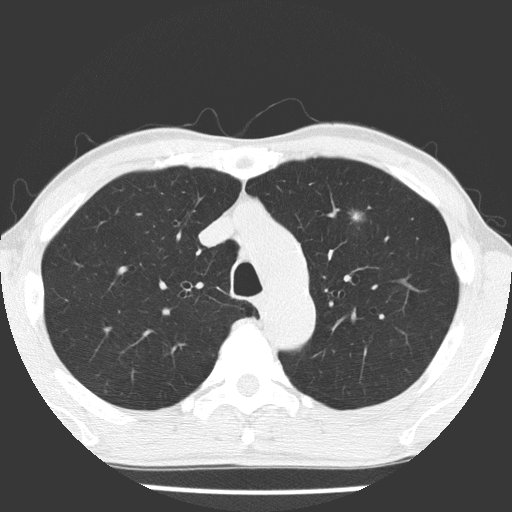
Axial slice from a low-dose chest CT screening exam; baseline annual screen; lung window (W 1500 / L -600 HU); 120 kVp; slice 51 of 177 in the series. Male participant, aged 66 years at enrolment.
Expert reader's lesion annotation, bounding box <330,197,378,242> (left, top, right, bottom; pixels). Screening reader's record for this exam (one nodule recorded; not confirmed to be the boxed lesion): non-calcified nodule or mass ≥4 mm, left upper lobe, 8 × 8 mm, poorly defined margins, mixed attenuation. Official screen result: positive, change unspecified: nodule(s) >= 4 mm or enlarging nodule(s), mass(es), or other non-specific abnormalities suspicious for lung cancer.